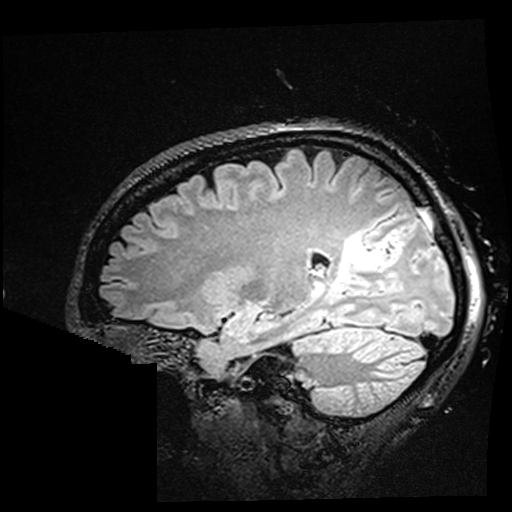
Brain MRI from a brain-tumour surgery series, one sagittal slice. Position 114 of 176 along the scan axis. T2 FLAIR. 512 × 512 image matrix, field of view 250 × 250 mm. Case-level facts recorded for this patient, not image findings: histopathology: Oligodendroglioma; WHO grade: 2; IDH mutation: yes; tumour location: Right Parietal.
Outlined on this slice (manually delineated by an expert):
- residual tumour: bounding box <332,231,389,292> (left, top, right, bottom; pixels)